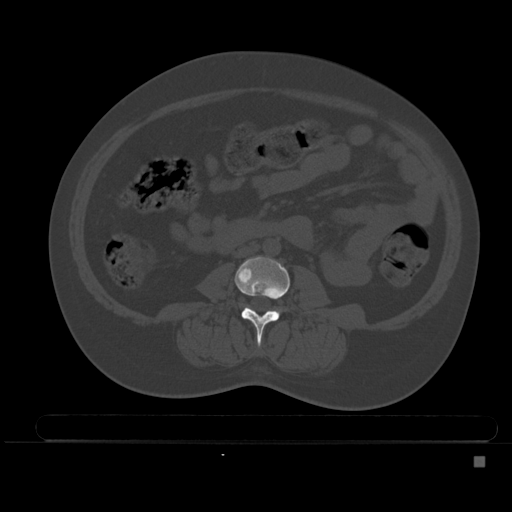
CT including the spine, one axial slice; position 147 of 495 along the scan axis; bone window (W 1800 / L 400 HU); 1.5 mm slice thickness; 512 × 512 image matrix. Patient: female, 33 years. From the clinical record (not read from this slice): primary cancer: breast.
Structures marked on this image (semi-automatic segmentation, software-assisted and operator-edited):
- L3 vertebra: box from (x=235, y=256) to (x=290, y=345) px